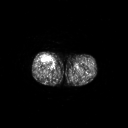
FDG PET of an extremity soft-tissue mass (from a PET/CT study), one axial slice; slice 263 of 311 in the series (ordered by position); 3.27 mm slice thickness; 128 × 128 image matrix, field of view 700 × 700 mm. Male patient, age 56 years. Case-level facts recorded for this patient, not image findings: histological type: pleiomorphic leiomyosarcoma; grade: intermediate; site of the primary tumour: right thigh.
Annotated regions visible in this slice (expert contour drawn on MRI and transferred to this co-registered scan by the dataset authors):
- gross tumour volume including surrounding oedema: bounding box (x1, y1, x2, y2) in pixels: (41, 55, 51, 62)
- gross tumour volume (mass): (43, 56, 48, 61)